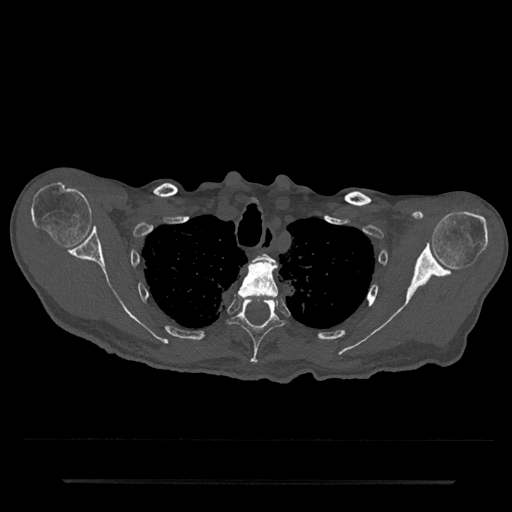
CT including the spine, one axial slice; position 634 of 797 along the scan axis; 120 kVp; bone window (W 1800 / L 400 HU); 0.5 mm slice thickness; 512 × 512 image matrix, field of view 427 × 427 mm. Patient: male, 74 years. From the clinical record (not read from this slice): primary cancer: prostate.
Annotated regions visible in this slice (semi-automatically segmented with operator editing):
- T2 vertebra: bounding box [x1, y1, x2, y2] px = [255, 253, 274, 262]
- T3 vertebra: [238, 260, 279, 297]
- T4 vertebra: [228, 298, 285, 364]